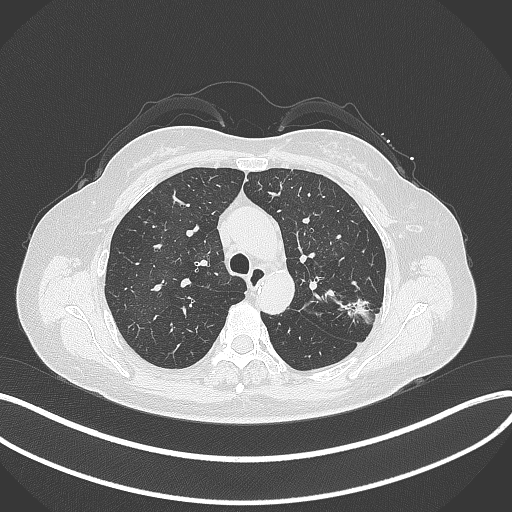
Chest CT, one axial slice. Slice 233 of 319 in the series (ordered by position). Reconstruction kernel B70f. Lung window (W 1500 / L -600 HU). 1 mm slice thickness. 512 × 512 image matrix. Female patient, age 60 years. From the clinical record (not read from this slice): clinical TNM (as recorded): T1c N0 M0.
Outlined on this slice (bounding box drawn by a radiologist):
- lung tumour (recorded histology: adenocarcinoma): box from (x=340, y=294) to (x=374, y=327) px